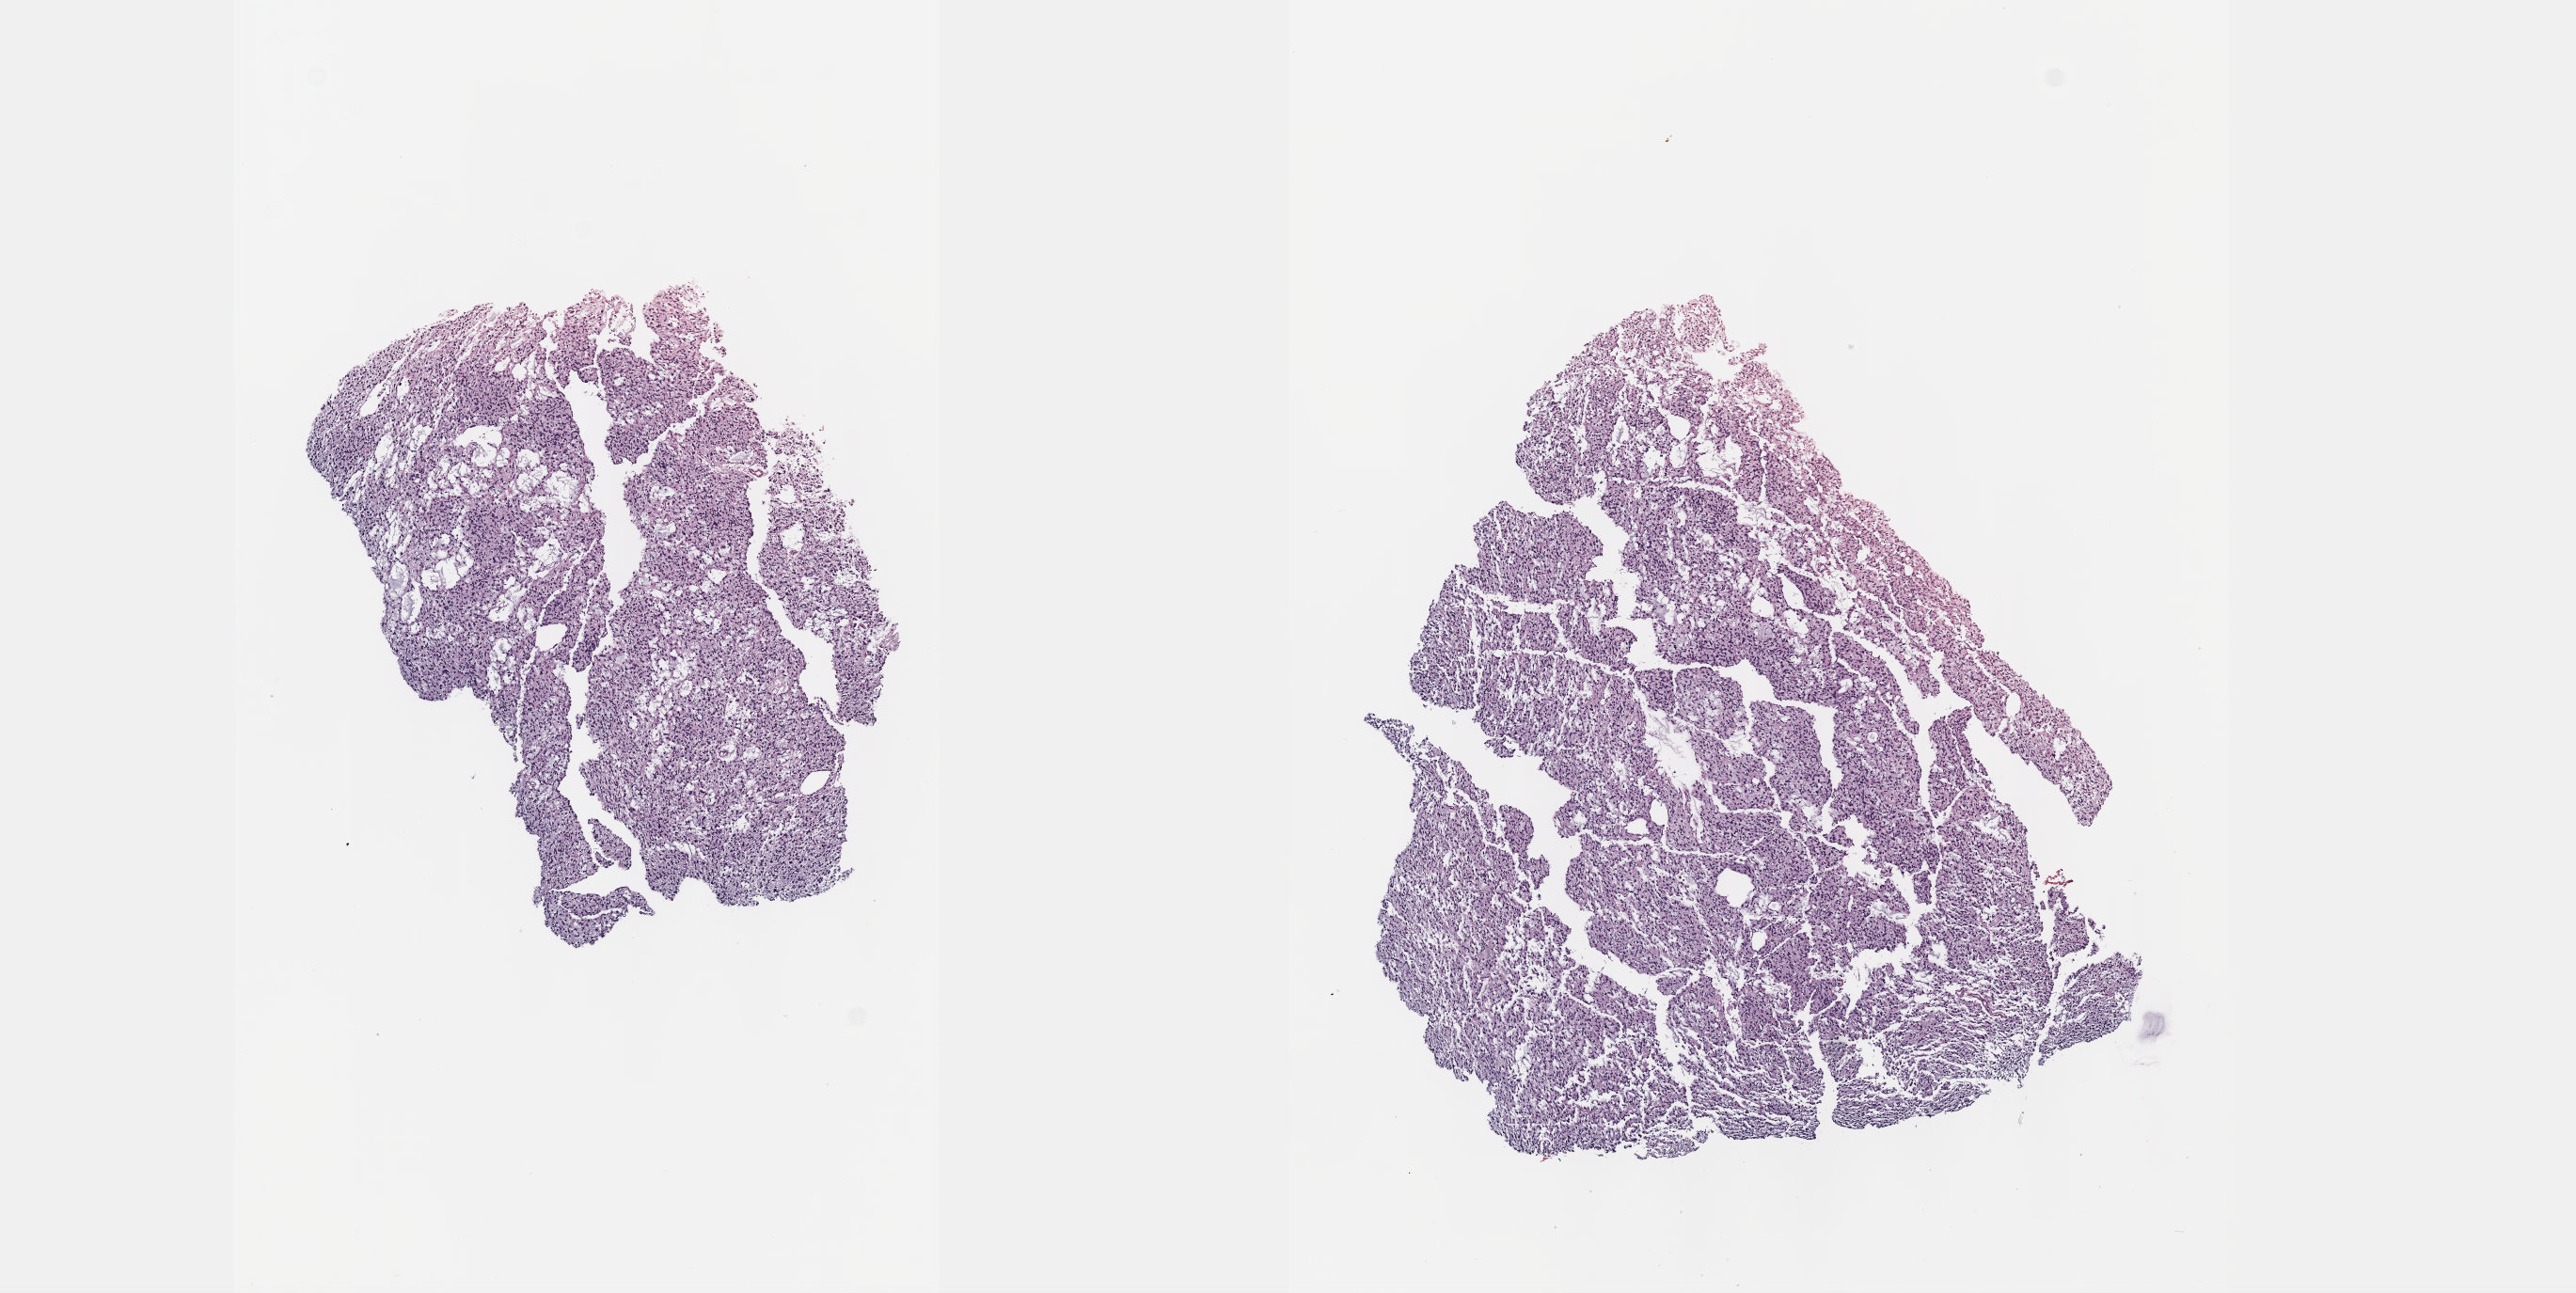
H&E-stained whole-slide image — a low-resolution overview of the entire scanned area, about 11.1 x 5.6 mm (acquisition: 40x scan); formalin-fixed paraffin-embedded (FFPE) diagnostic section; sample: primary tumour, brain. Patient: female, age at initial diagnosis 41 years. Histologic grade: G2 (moderately differentiated).
Diagnosis: Oligodendroglioma, NOS (cerebrum). Laterality: right.